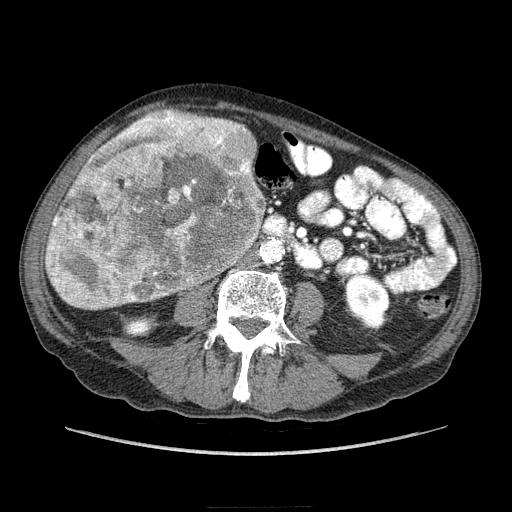
Contrast-enhanced abdominal CT (liver protocol), one axial slice; position 61 of 218 along the scan axis; 100 kVp; soft-tissue window (W 400 / L 40 HU); 2.5 mm slice thickness; 512 × 512 image matrix, field of view 380 × 380 mm. Case-level facts recorded for this patient, not image findings: diagnosis: hepatocellular carcinoma (patient treated with transarterial chemoembolisation; whether this scan precedes or follows treatment is not stated here); TNM stage (as recorded): Stage-IIIA; Child-Pugh class: A; tumour differentiation: well differentiated; tumour nodularity: multinodular.
Structures marked on this image (semi-automatically segmented with operator editing):
- liver parenchyma outside the tumour (the mass and vessels are separate outlines, so this box may not span the whole liver): bounding box <46,122,256,310> (left, top, right, bottom; pixels)
- mass: <47,110,266,310>